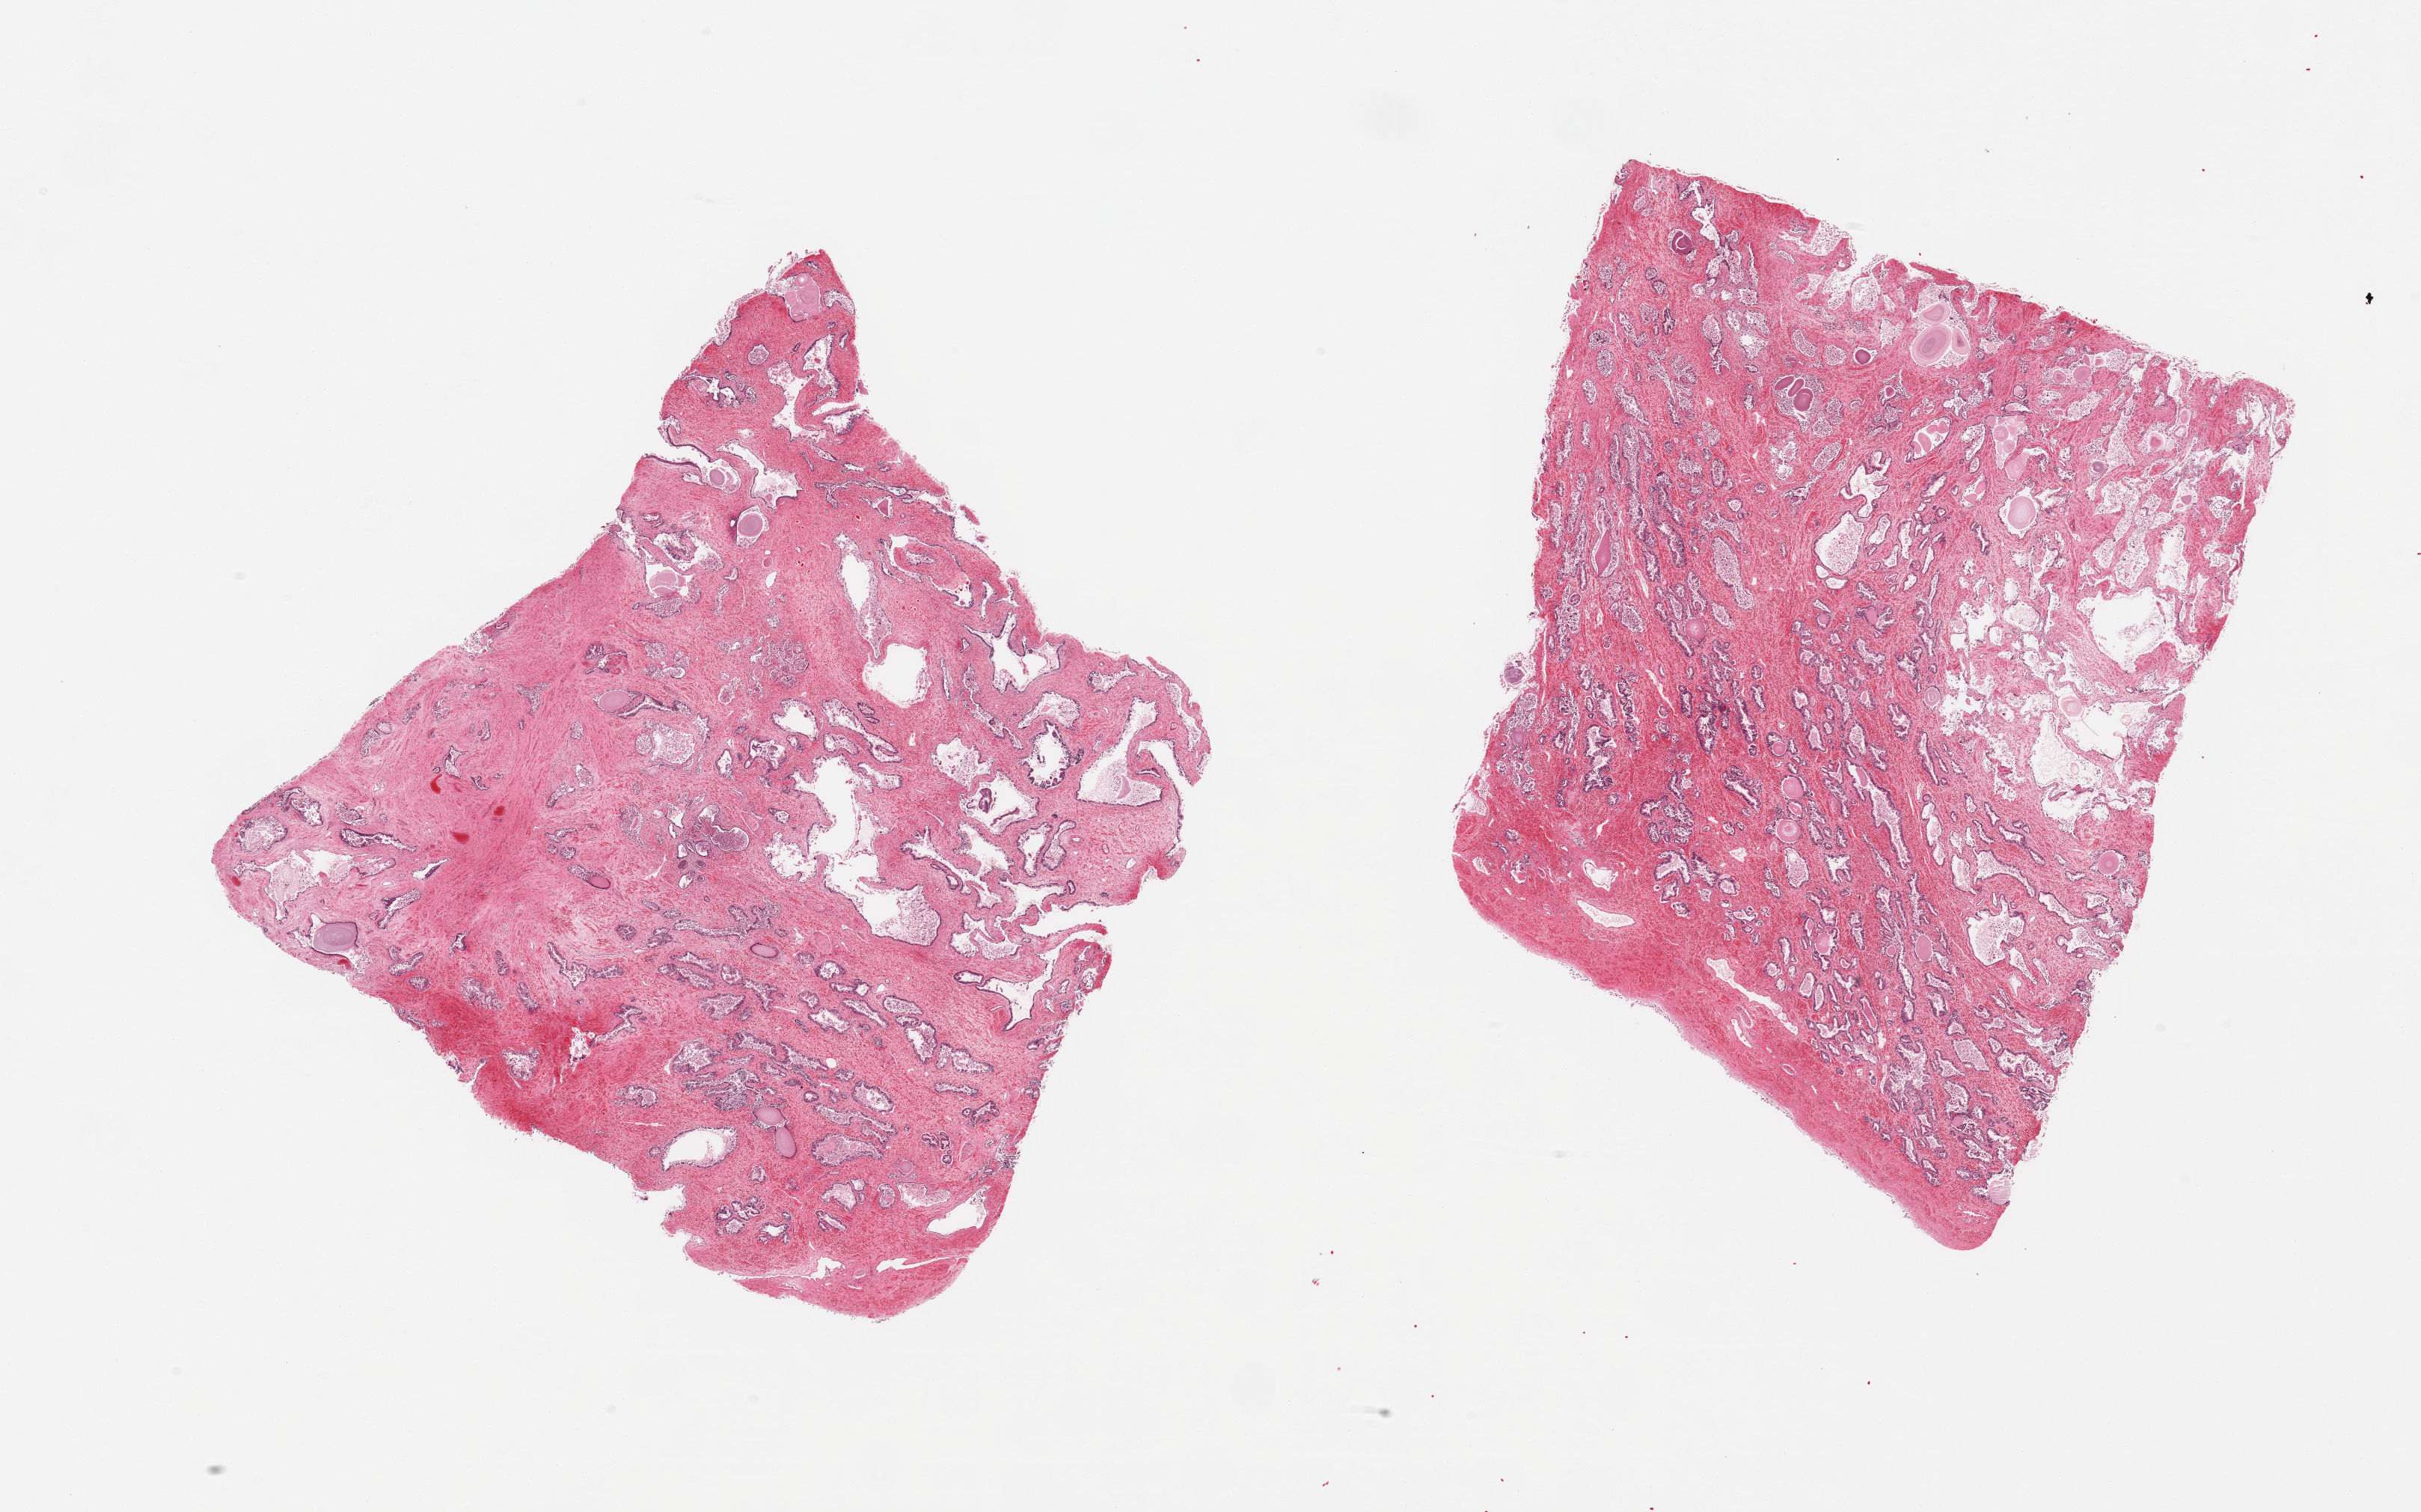
Digitized haematoxylin and eosin-stained section, whole scanned area (about 25.6 x 16.0 mm) shown as a low-resolution overview; PAXgene-fixed paraffin-embedded (PFPE) section; target tissue: prostate; donor tissue sample. Donor sex: male.
Pathologist's review note for this sample: 2 pieces.